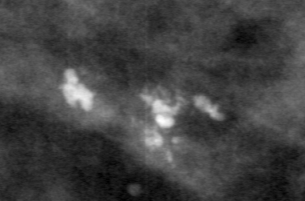
Crop from a digitized film mammogram around one marked abnormality, right breast, CC view.
- Marked abnormality: calcifications, morphology dystrophic, distribution clustered; BI-RADS assessment category 3; pathology result (as recorded, not read from the image): benign.